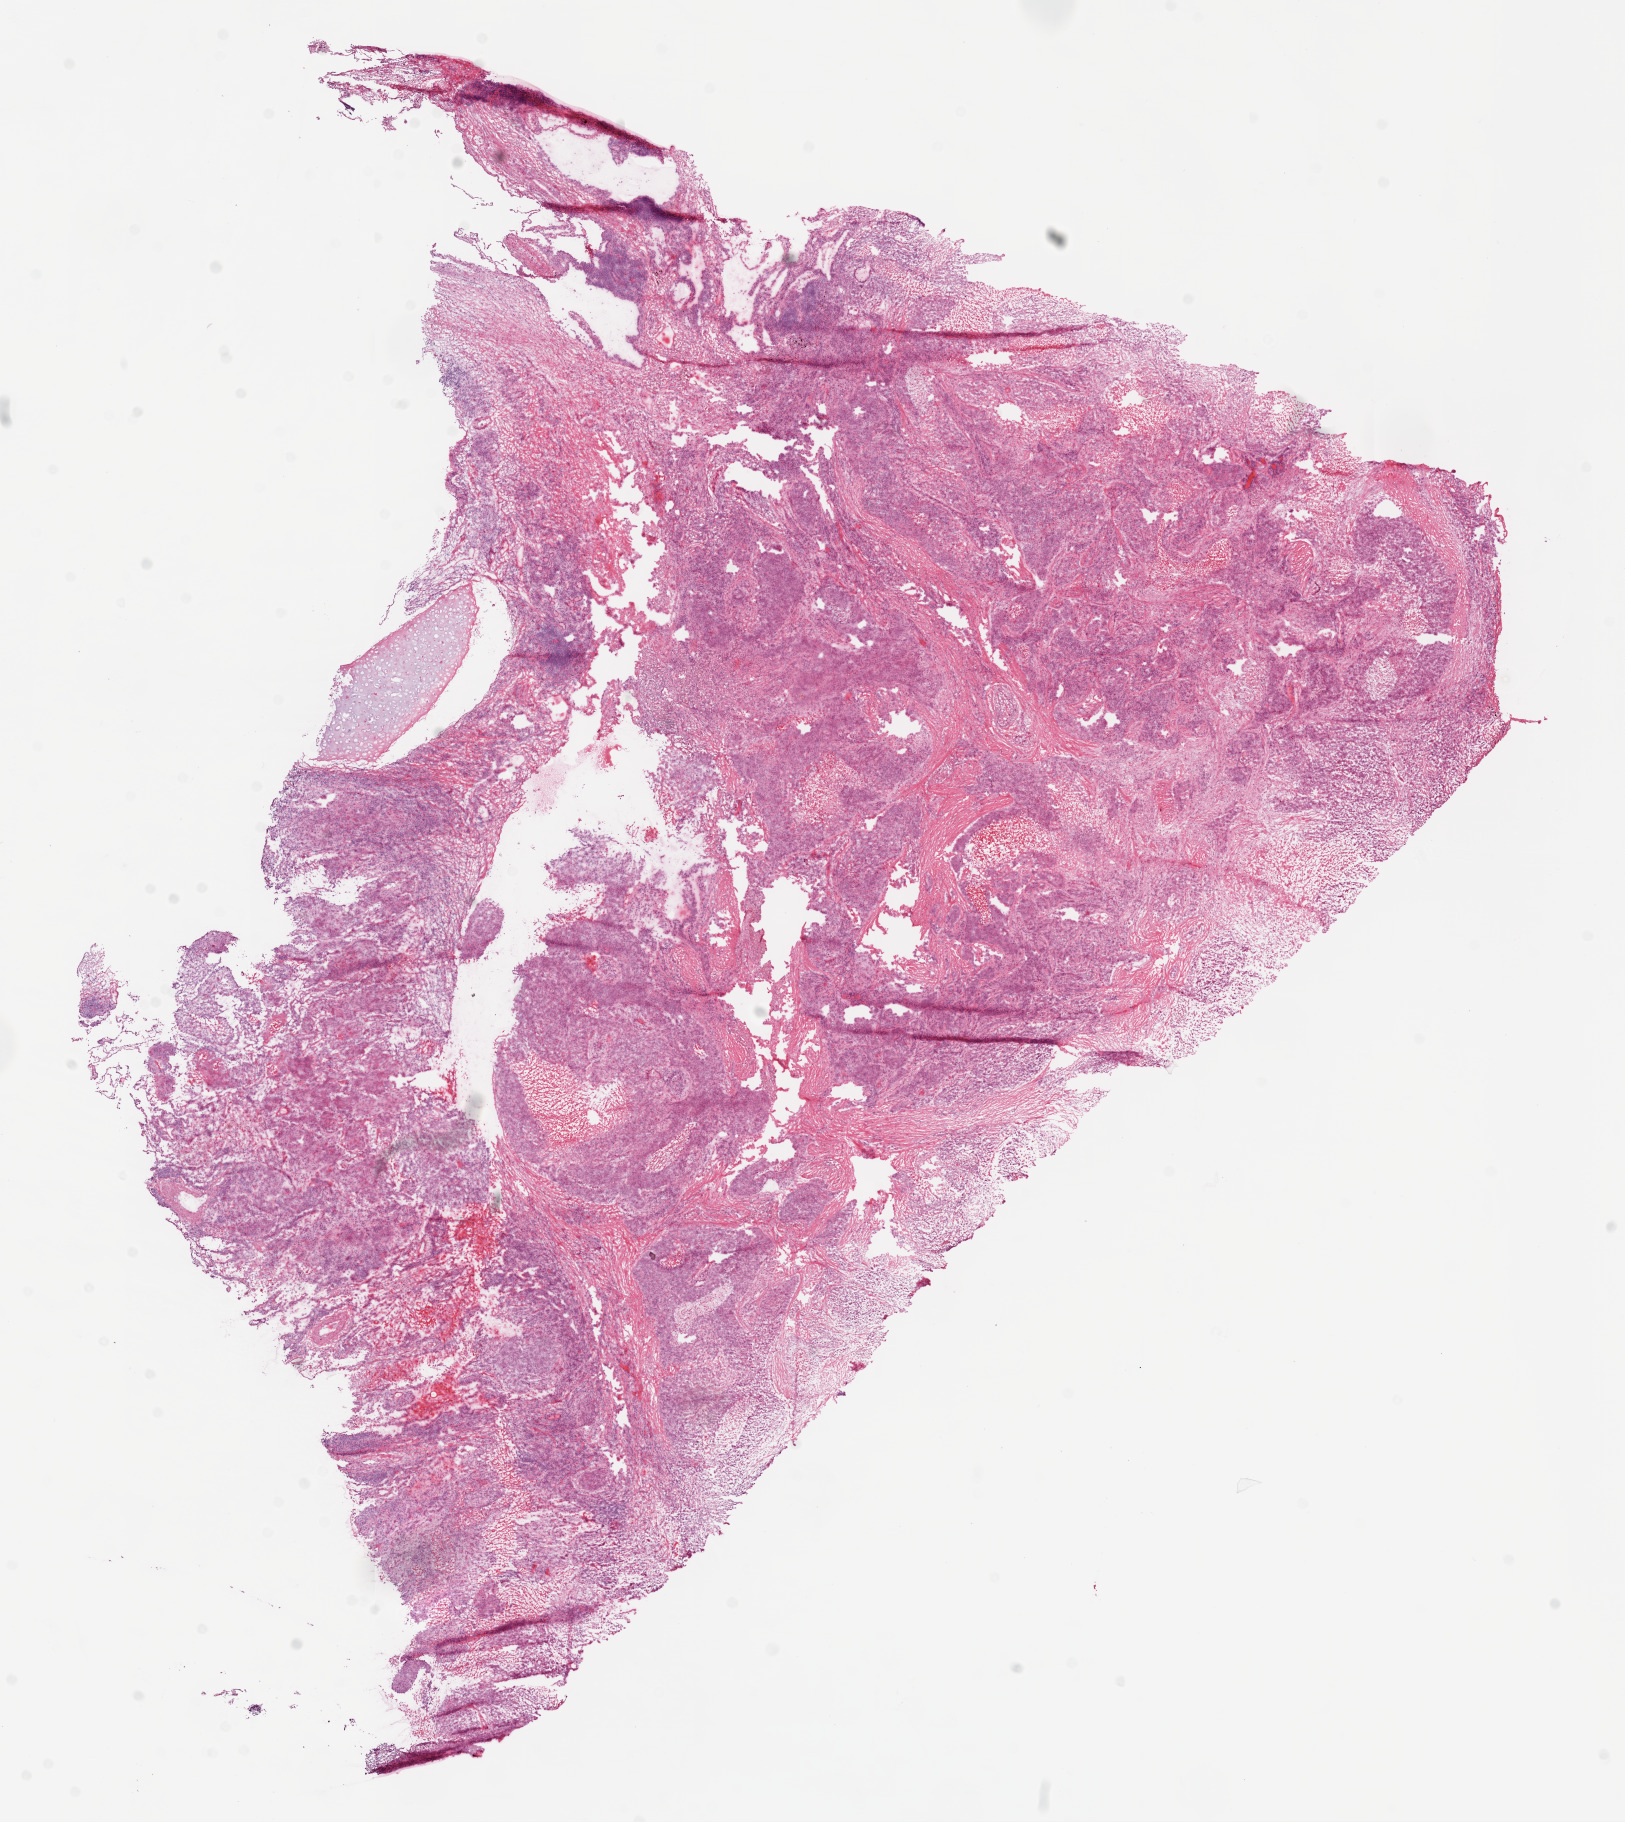
Digitized H&E-stained tissue section (whole slide) — shown as a low-resolution overview of the whole scanned area (about 13.0 x 14.6 mm); frozen section from the top of the tissue portion; lung, primary tumour sample. Male, age 64 years at initial diagnosis. Slide review estimates, as recorded: tumour cells 66%, tumour nuclei 65%, normal cells 11%, stromal cells 17%, necrosis 6%. Inflammatory infiltration, as recorded: lymphocyte infiltration 15%, monocyte infiltration 0%, neutrophil infiltration 0%.
AJCC pathologic stage: IA. Diagnosis: Squamous cell carcinoma, NOS (upper lobe, lung). TNM: T1b N0 M0.